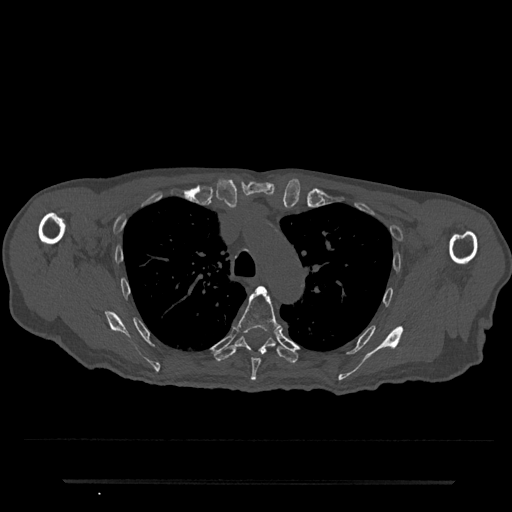
CT including the spine, one axial slice; bone window (W 1800 / L 400 HU); 0.5 mm slice thickness; 512 × 512 image matrix, field of view 427 × 427 mm. Male patient, age 74 years. Case-level facts recorded for this patient, not image findings: primary cancer: prostate.
Annotated regions visible in this slice (semi-automatic segmentation, software-assisted and operator-edited):
- T5 vertebra: box from (x=237, y=286) to (x=282, y=381) px
- T6 vertebra: (x=214, y=336)–(x=298, y=364)